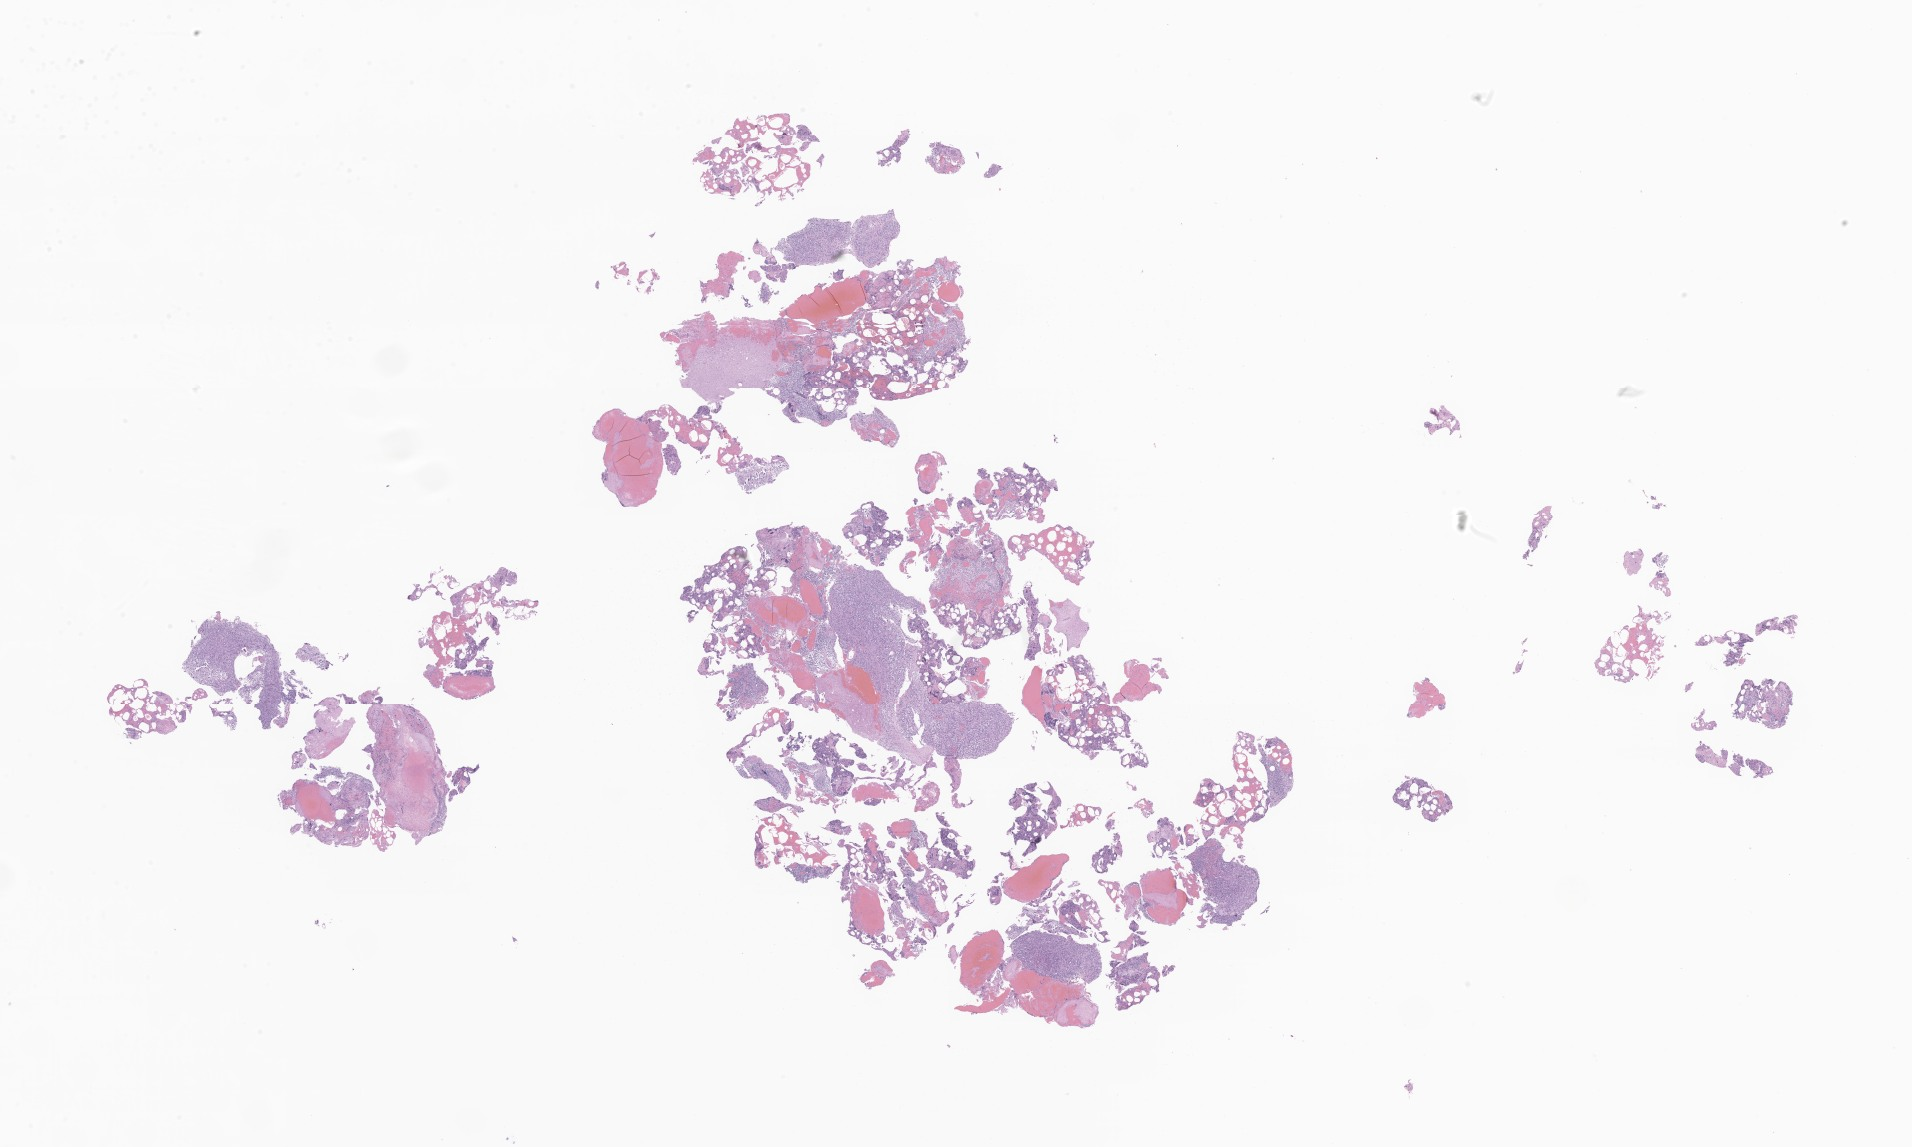
Digitized hematoxylin and eosin (H&E)-stained section of tumor tissue from the brain — shown as a low-resolution overview of the whole scanned area (about 32.2 x 19.3 mm). FFPE section. Patient: female, age 115 months (9 years 7 months).
* recorded diagnosis: Neoplasm, uncertain whether benign or malignant